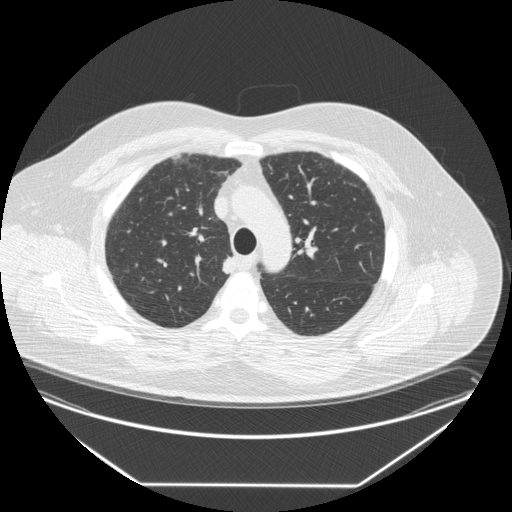
Low-dose screening chest CT, one axial slice; position 201 of 258 along the scan axis; 120 kVp; lung window (W 1500 / L -600 HU); 2.5 mm slice thickness; 512 × 512 image matrix, field of view 440 × 440 mm.
Annotated regions visible in this slice (manually delineated by an expert):
- lesion 1 (tumor, upper lobe of right lung): bounding box (x1, y1, x2, y2) in pixels: (223, 256, 237, 274)